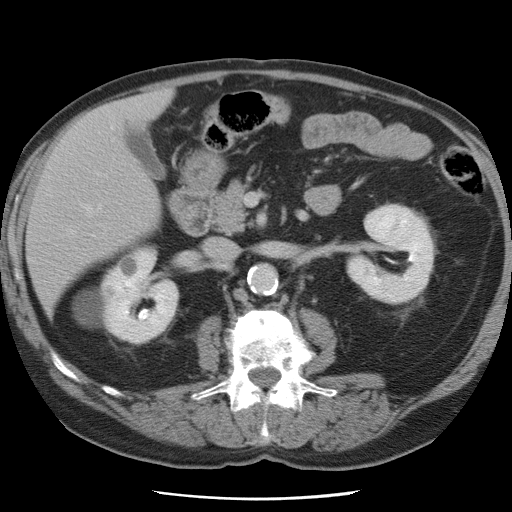
Contrast-enhanced abdominal CT, one axial slice; position 32 of 78 along the scan axis; 120 kVp; intravenous contrast given; soft-tissue window (W 400 / L 40 HU); 5 mm slice thickness; 512 × 512 image matrix, field of view 337 × 337 mm. Male patient, age 75 years. Case-level facts recorded for this patient, not image findings: diagnosis: colorectal cancer liver metastases, imaged before liver resection; multiple liver metastases: yes; largest metastasis: 2.4 cm; disease in both lobes: yes.
Annotated regions visible in this slice (manually delineated by an expert):
- hepatic veins: bounding box <68,205,101,233> (left, top, right, bottom; pixels)
- liver: <28,92,169,312>
- planned liver remnant (the part of the liver to remain after resection): <28,116,160,311>